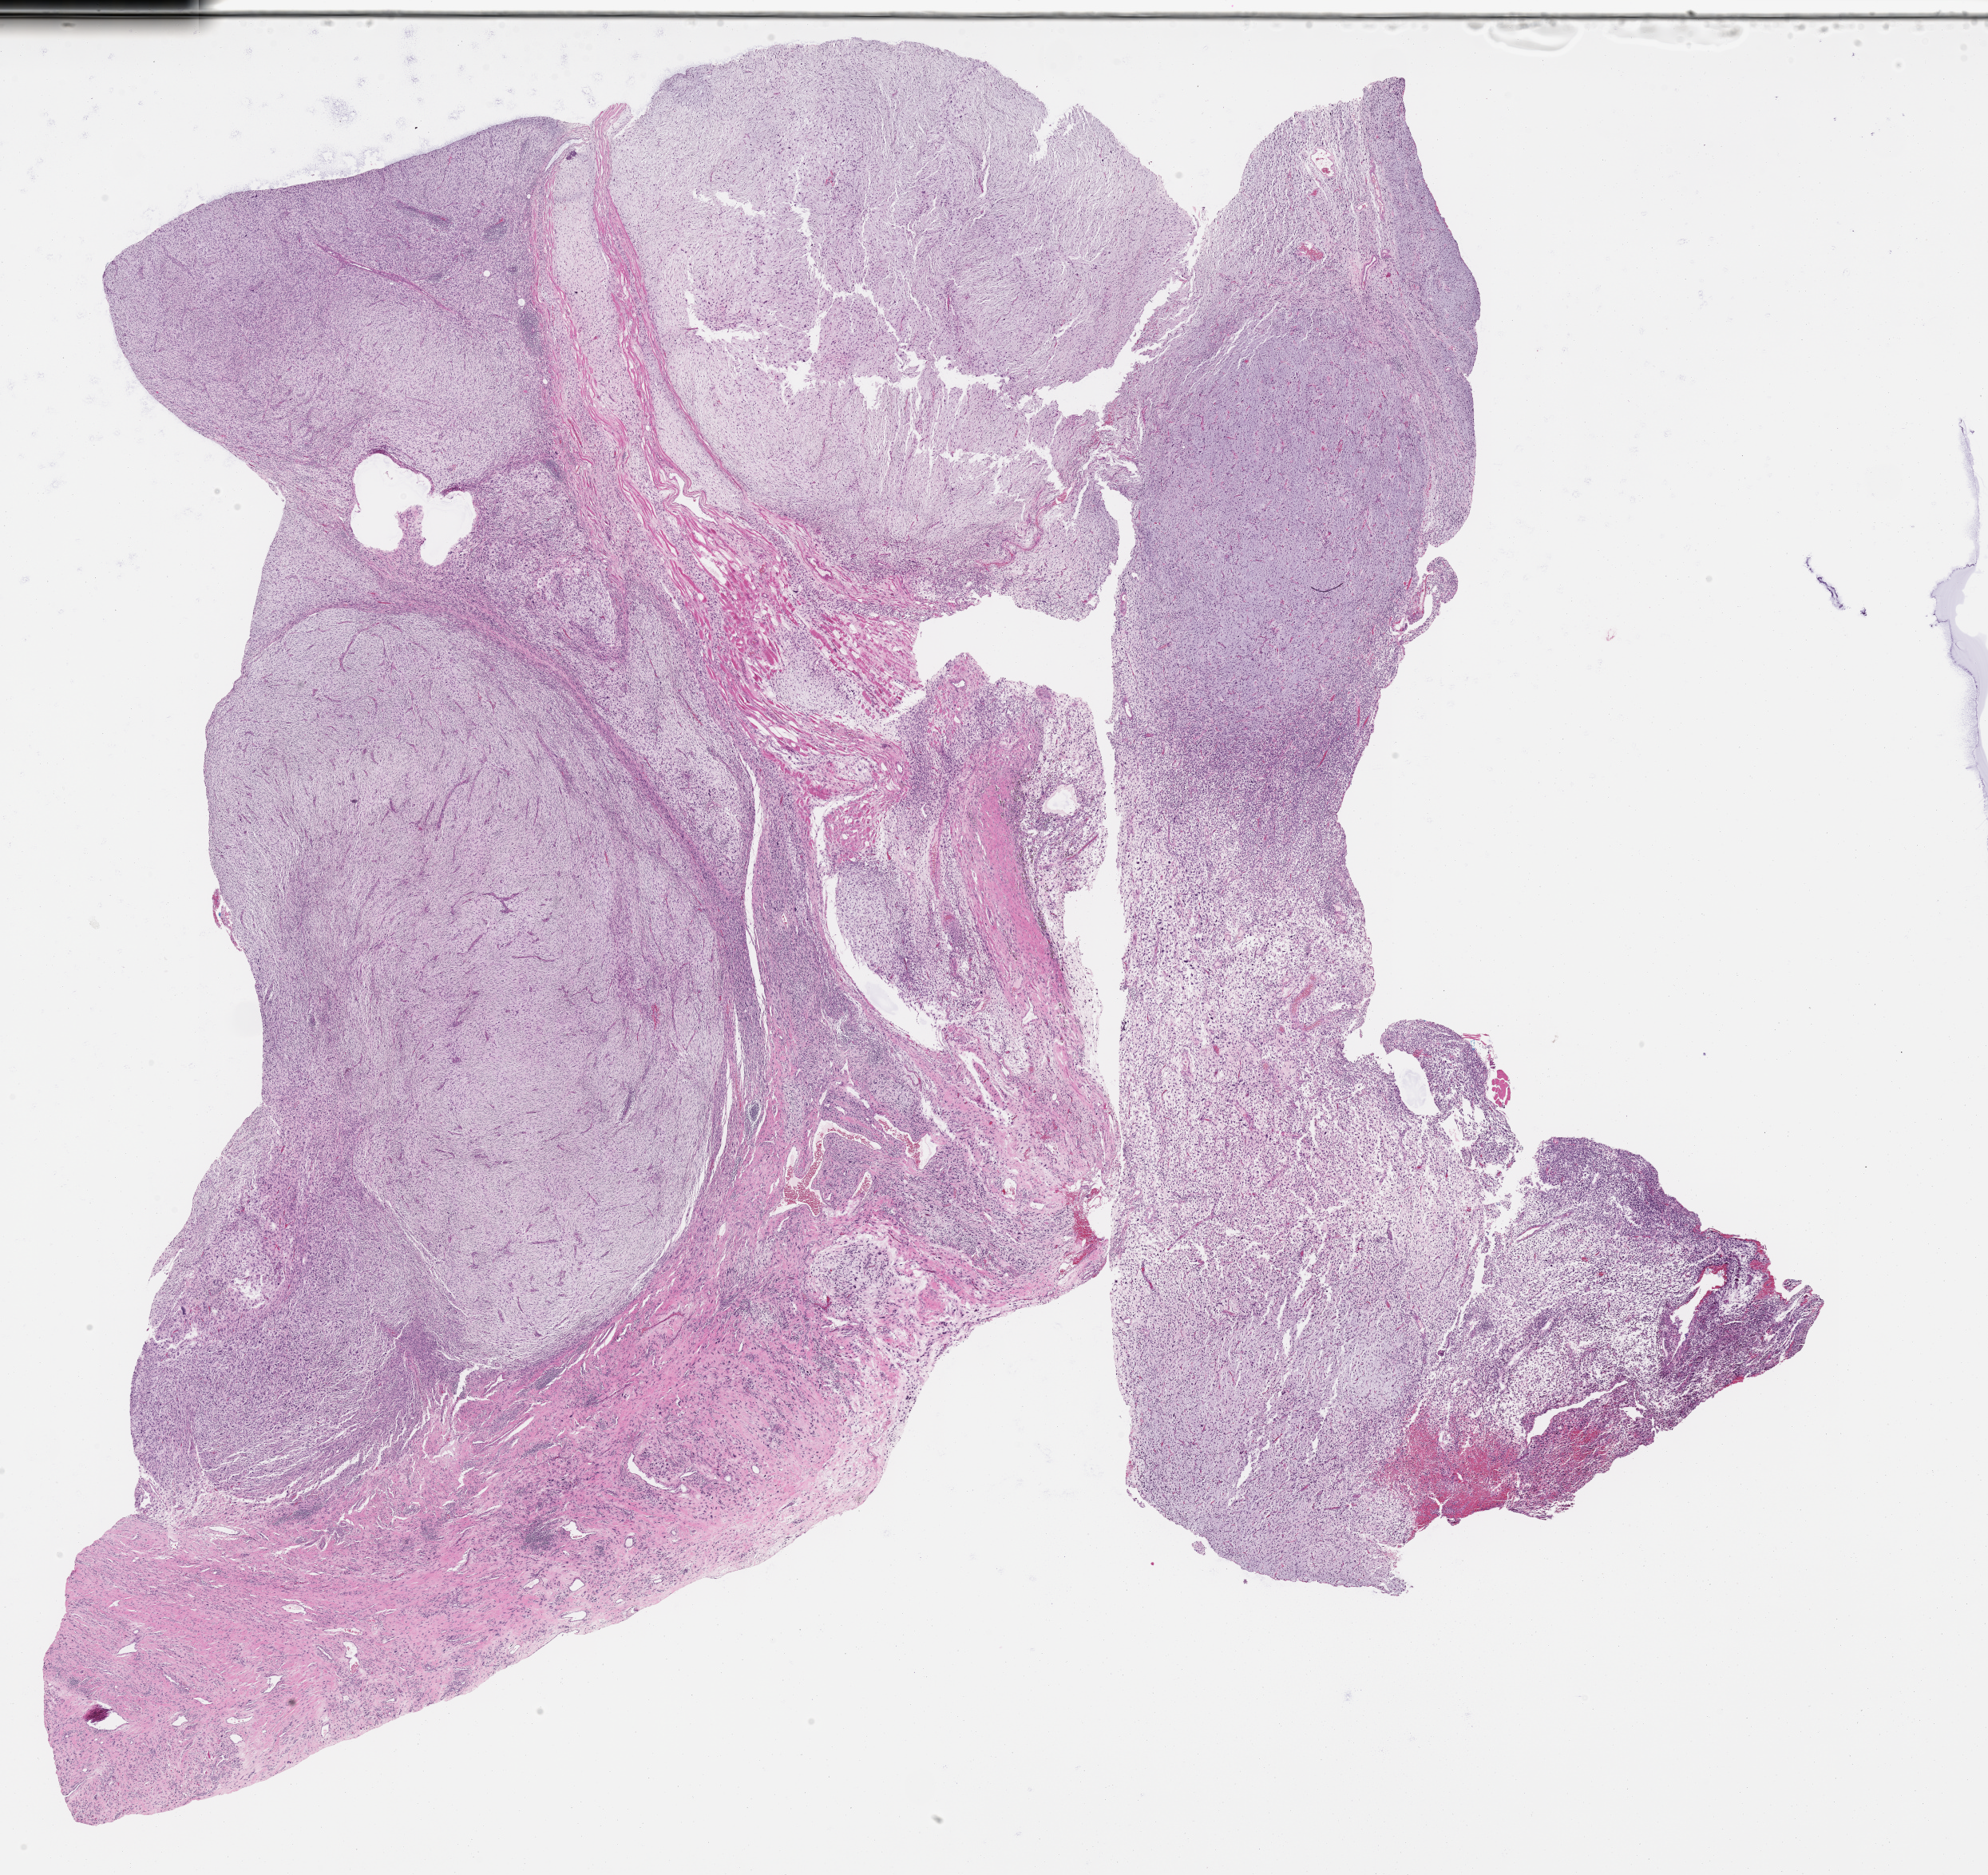
Digitized H&E tissue section (whole slide) — whole scanned area (about 20.1 x 19.0 mm, from a 40x scan) shown as a low-resolution overview; formalin-fixed paraffin-embedded (FFPE) diagnostic section; primary tumour sample from the connective, subcutaneous and other soft tissues. Male, age 61 years at initial diagnosis.
Diagnosis: Fibromyxosarcoma (connective, subcutaneous and other soft tissues of pelvis).